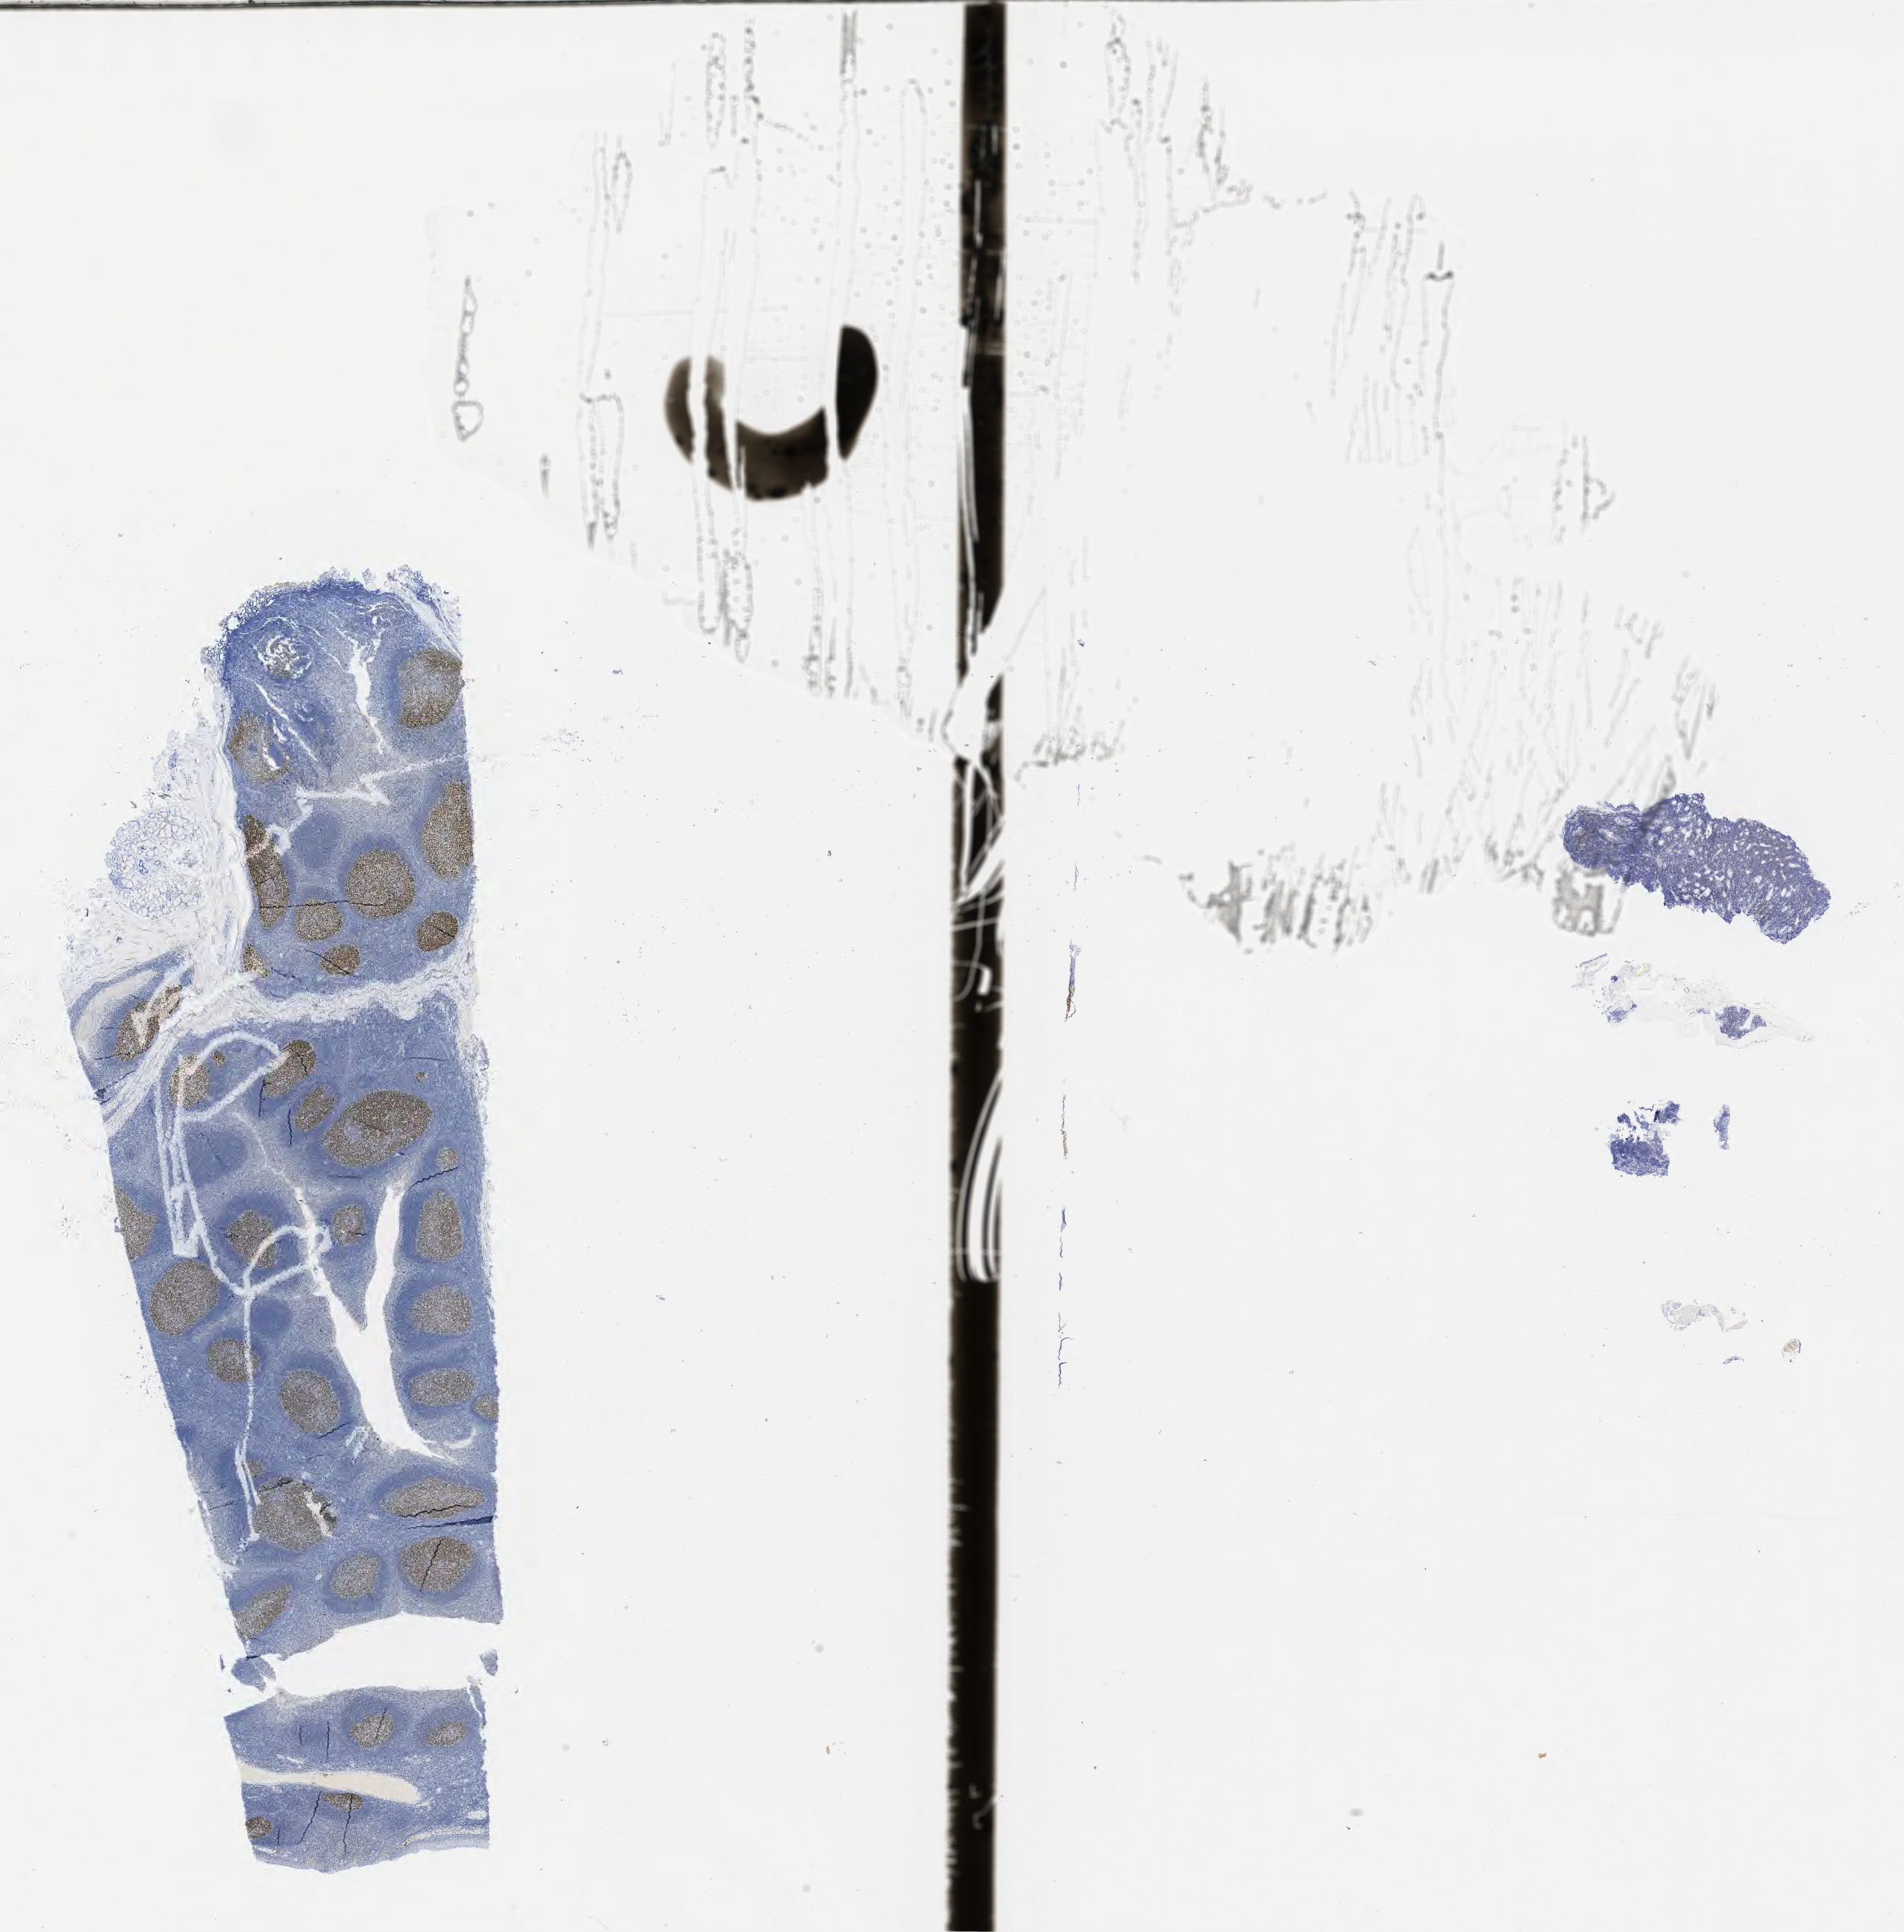
Whole-slide image, immunohistochemical stain for BCL6, low-resolution overview of the scanned area, about 20.6 x 20.9 mm; specimen: tumor tissue; site: stomach. Female patient, age 28 years.
* diagnosis: Burkitt lymphoma, NOS